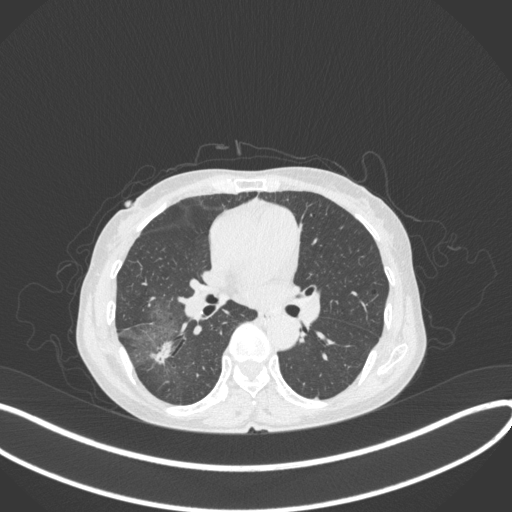
Chest CT, one axial slice; slice 211 of 379 in the series (ordered by position); reconstruction kernel B31f; 120 kVp; lung window (W 1500 / L -600 HU); 512 × 512 image matrix, field of view 400 × 400 mm. Female patient, age 69 years. From the clinical record (not read from this slice): clinical TNM (as recorded): T1b N0 M0; histopathological grade: G2-3.
Structures marked on this image (bounding box drawn by a radiologist):
- lung tumour (recorded histology: adenocarcinoma): box from (x=148, y=334) to (x=179, y=366) px